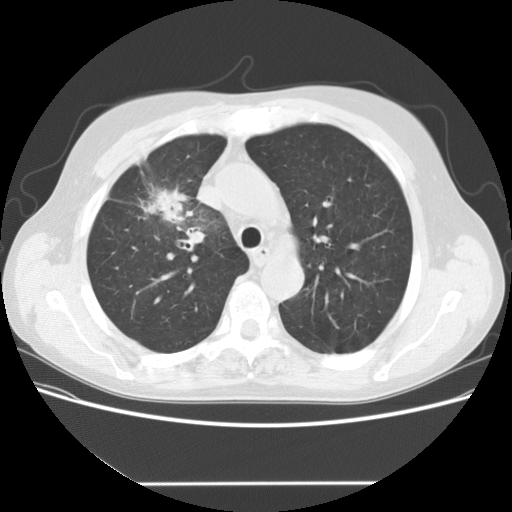
Low-dose screening chest CT, one axial slice. Slice 111 of 153 in the series (ordered by position). Reconstruction kernel STANDARD. Lung window (W 1500 / L -600 HU). 2.5 mm slice thickness. 512 × 512 image matrix, field of view 360 × 360 mm.
Structures marked on this image (expert manual segmentation):
- lesion 1 (tumor, upper lobe of right lung): bounding box (x1, y1, x2, y2) in pixels: (144, 188, 194, 225)